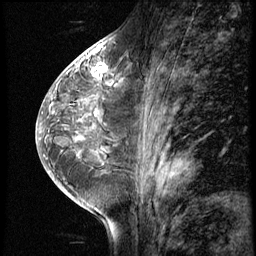
Breast MRI (dynamic contrast-enhanced), one sagittal slice; 3 images stored at this slice position (order not interpretable as contrast timing); 1.5 T; TE 4.2 ms, TR 8.9 ms; 2.5 mm slice thickness; 256 × 256 image matrix, field of view 200 × 200 mm. Patient: female, 38 years. From the clinical record (not read from this slice): setting: breast cancer imaged before/during neoadjuvant chemotherapy; receptor status: triple-negative.
Outlined on this slice (semi-automatically segmented with operator editing):
- analysis volume of interest (the breast-tissue region the enhancement analysis was run in; not a lesion): bounding box [x1, y1, x2, y2] px = [88, 60, 110, 84]
- tumour enhancement mask (voxels above the 140 % enhancement threshold inside the analysis volume of interest): [92, 63, 104, 75]